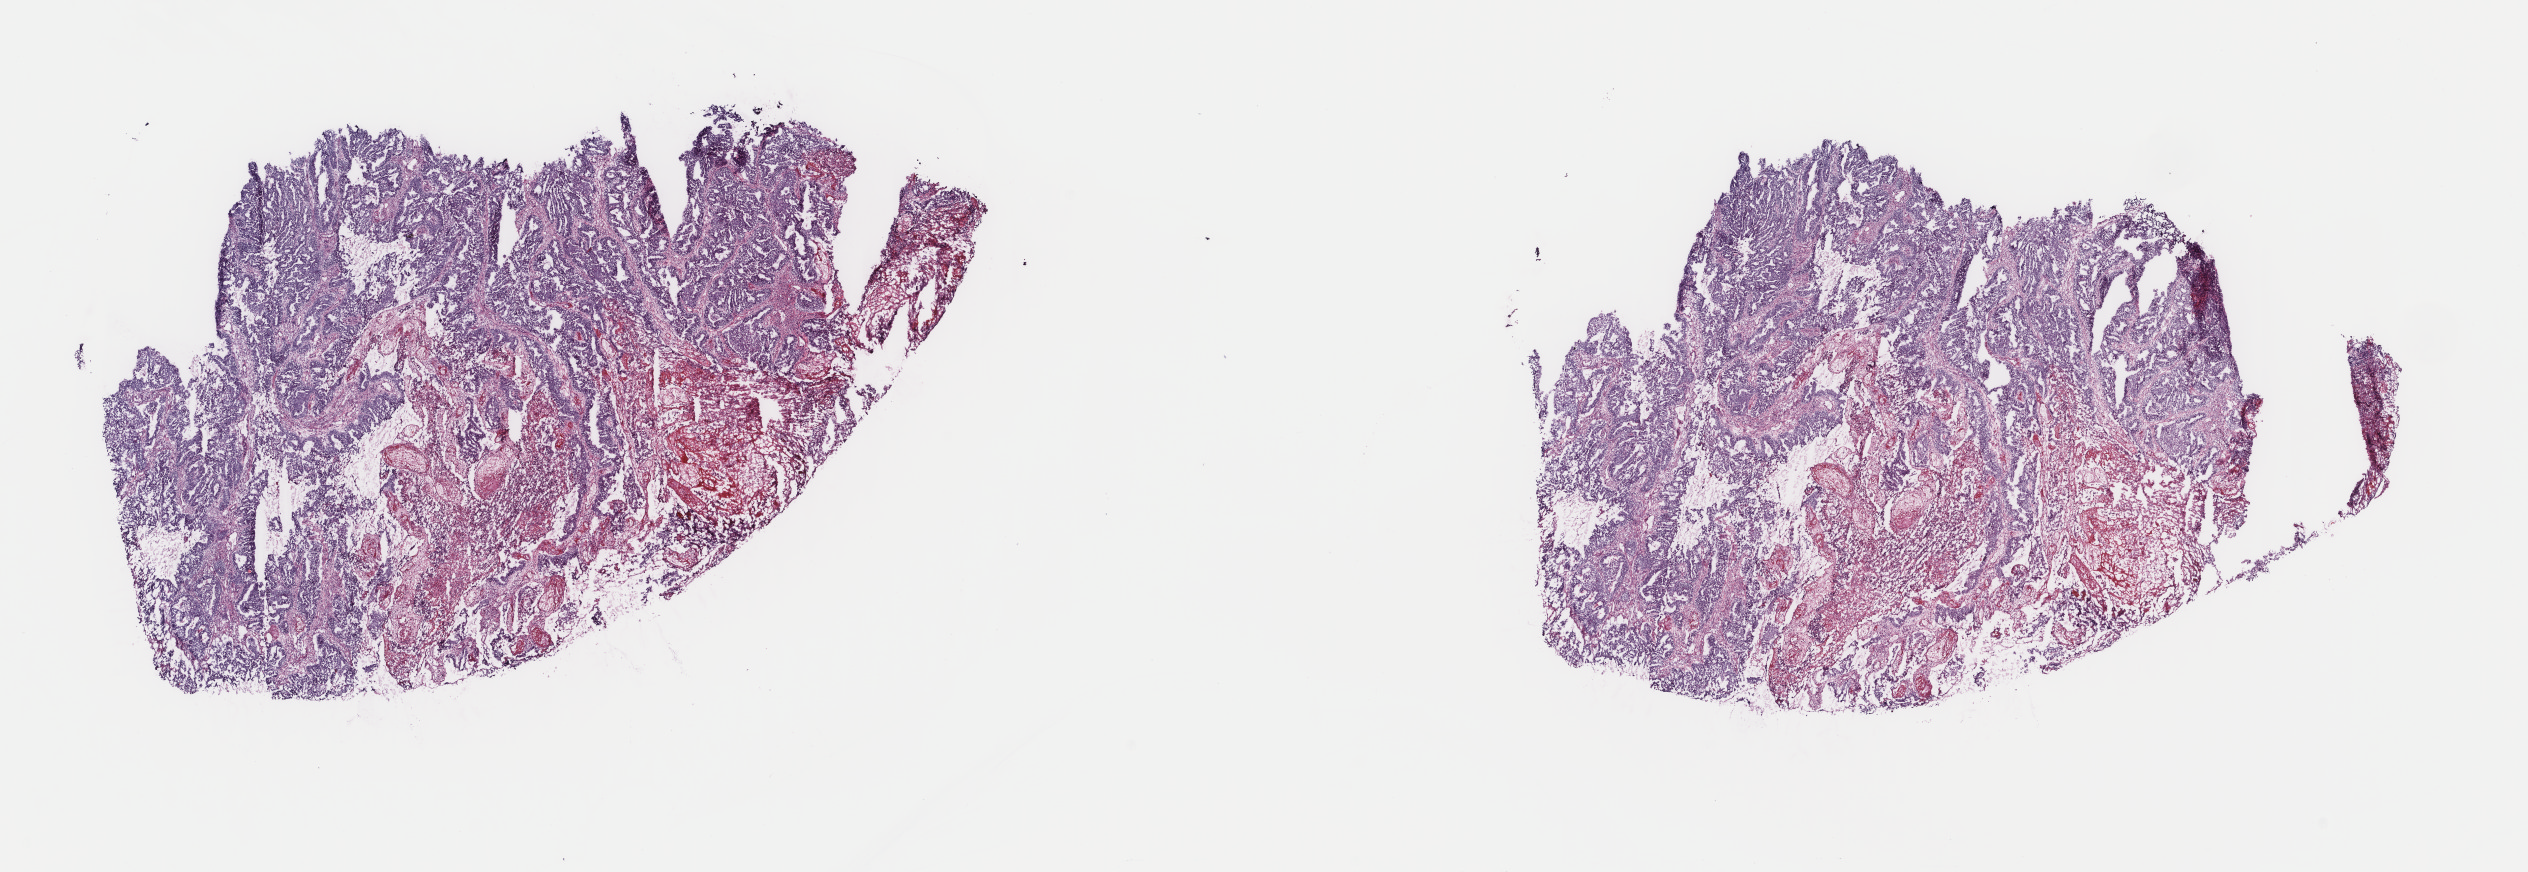
H&E-stained whole-slide image, whole scanned area (about 20.1 x 6.9 mm) shown as a low-resolution overview. Frozen section from the top of the tissue portion. Uterus, primary tumour sample. Patient: female, age at initial diagnosis 86 years. Histologic grade: G2 (moderately differentiated). Pathologist review of this section (percent, as recorded): tumour cells 80%, tumour nuclei 80%, normal cells 0%, stromal cells 15%, necrosis 5%. Inflammatory infiltration, as recorded: lymphocyte infiltration 40%, monocyte infiltration 20%, neutrophil infiltration 20%.
* FIGO stage: IIIB
* pathologic diagnosis: Endometrioid adenocarcinoma, NOS (isthmus uteri)